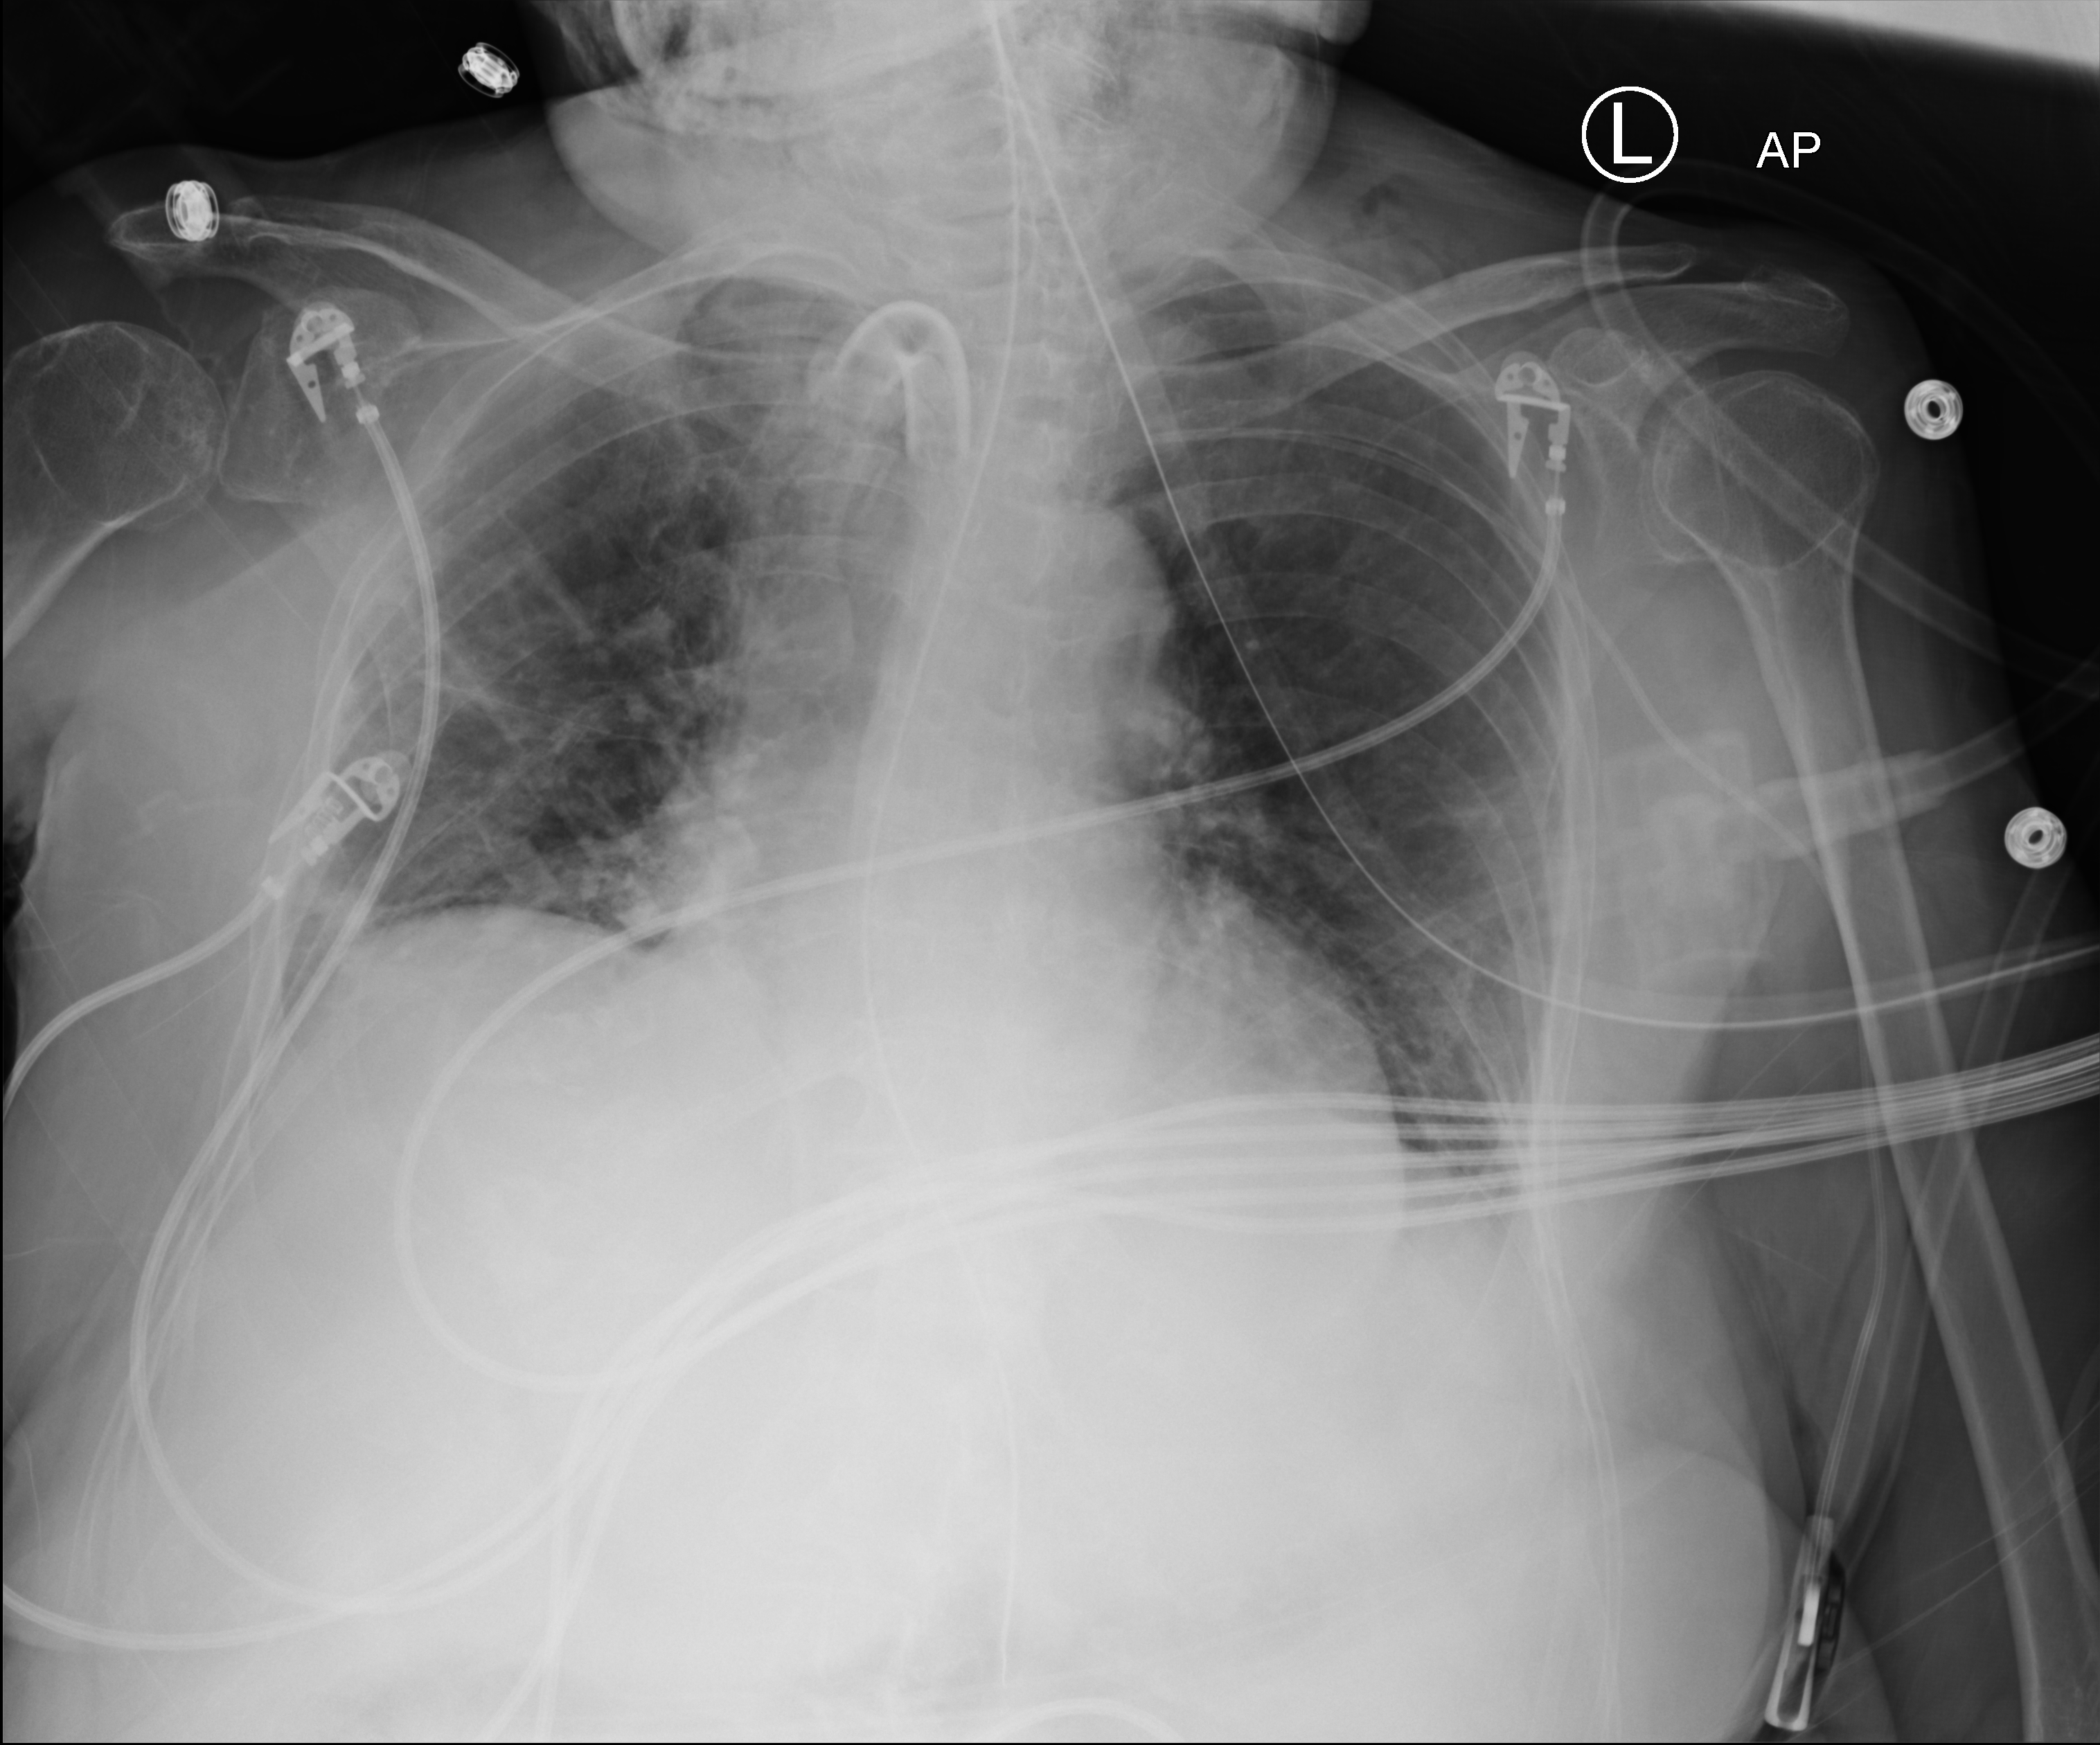
Chest X-ray (portable), anteroposterior (AP) projection. Female patient hospitalised with COVID-19, age 75–90 years.
From the hospital-stay record, not from the radiograph (when in the stay this image was taken is not recorded): hypertension (admission record): yes; mechanically ventilated during this hospital stay: yes; diabetes (admission record): no.